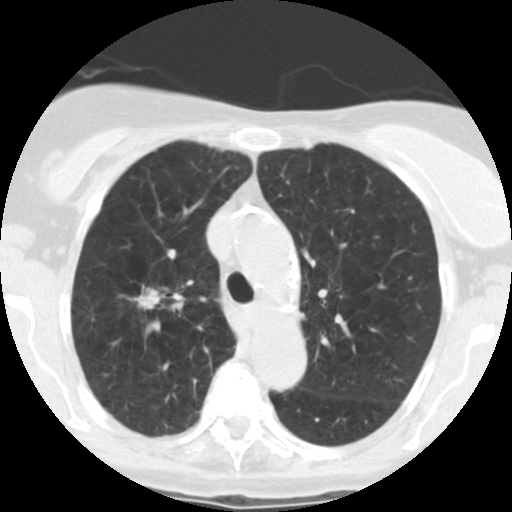
Chest CT (low-dose screening protocol), one axial image; first (baseline) screen; lung window (W 1500 / L -600 HU); slice 180 of 246 in the series. Female participant, aged 67 years at enrolment.
Expert reader's lesion annotation, bounding box (x1, y1, x2, y2) in pixels: (114, 278, 175, 319). The screening reader recorded 6 non-calcified nodules or masses ≥4 mm on this exam; which of them this box marks is not recorded. Official screen result: positive, change unspecified: nodule(s) >= 4 mm or enlarging nodule(s), mass(es), or other non-specific abnormalities suspicious for lung cancer. Participant outcome: lung cancer diagnosed 15 days after this screen — adenocarcinoma, NOS, right upper lobe, moderately differentiated (G2), stage IA (AJCC 6th edition), 14 mm at pathology.